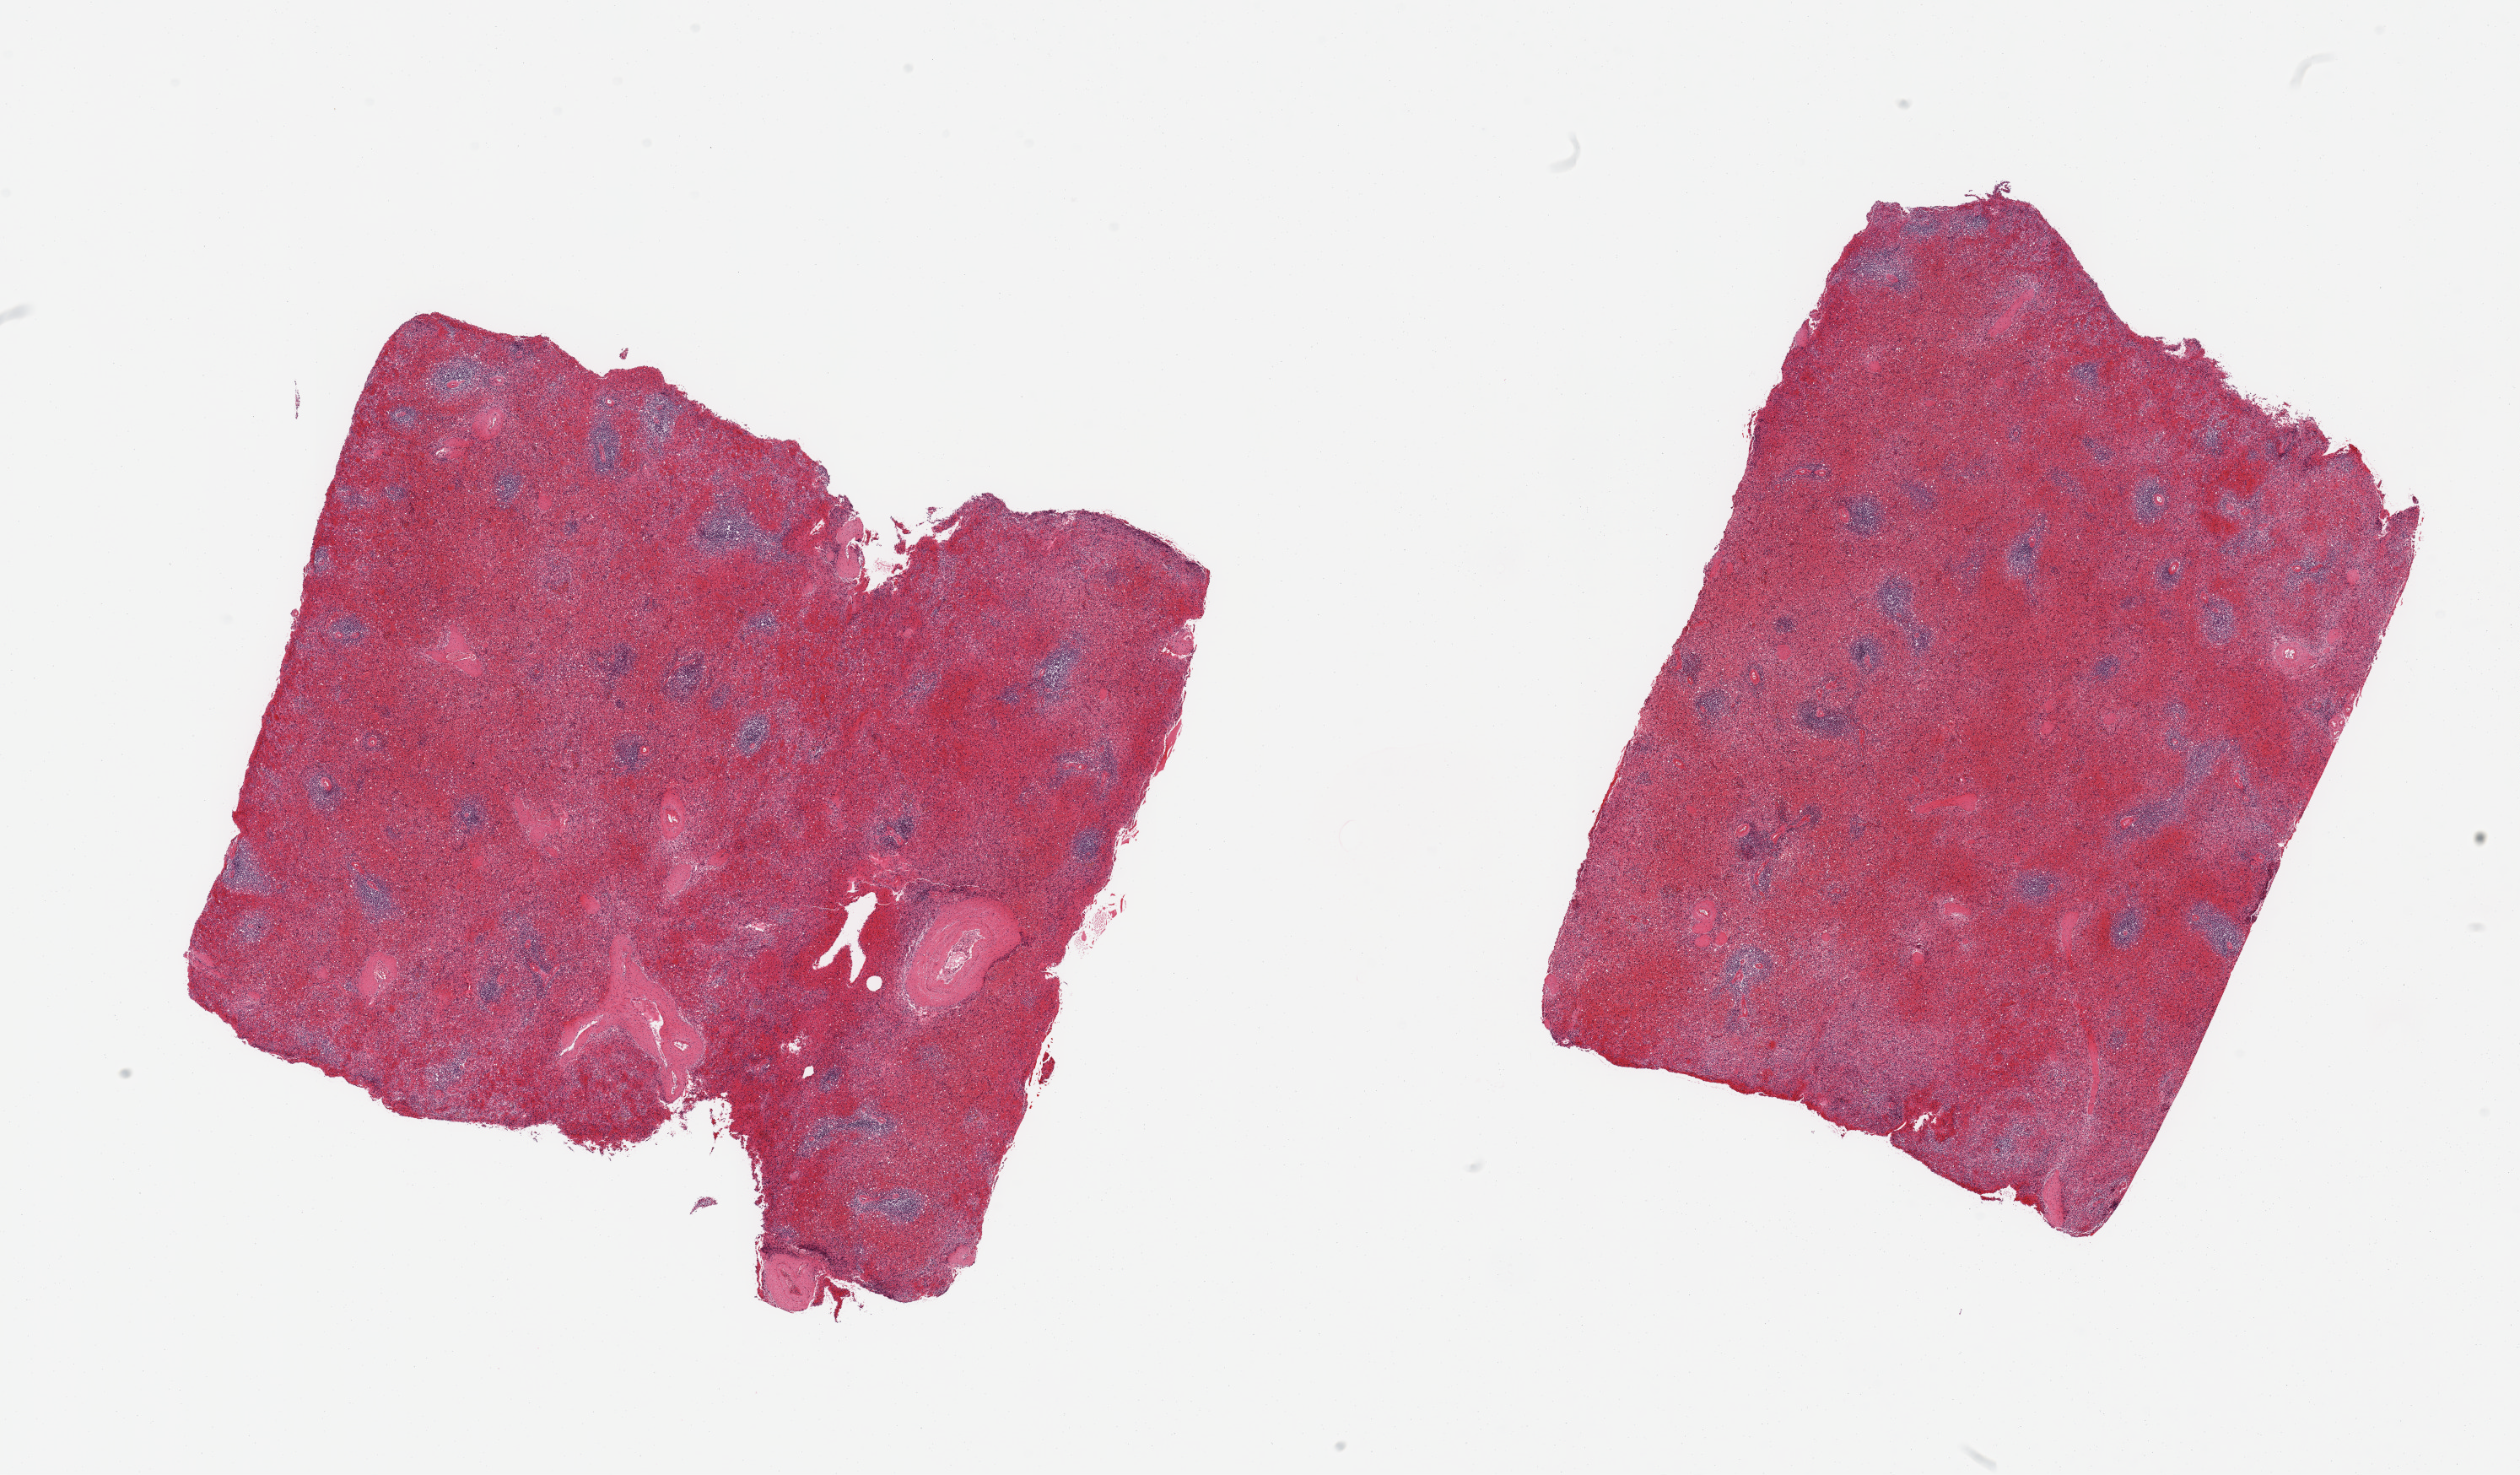
Haematoxylin and eosin whole-slide image, brightfield — whole scanned area (about 23.6 x 13.8 mm, from a 20x scan) shown as a low-resolution overview, PAXgene-fixed, paraffin-embedded tissue, sampled site (target tissue): spleen, tissue donor sample.
* pathologist's review note for this sample: 2 pieces; congested